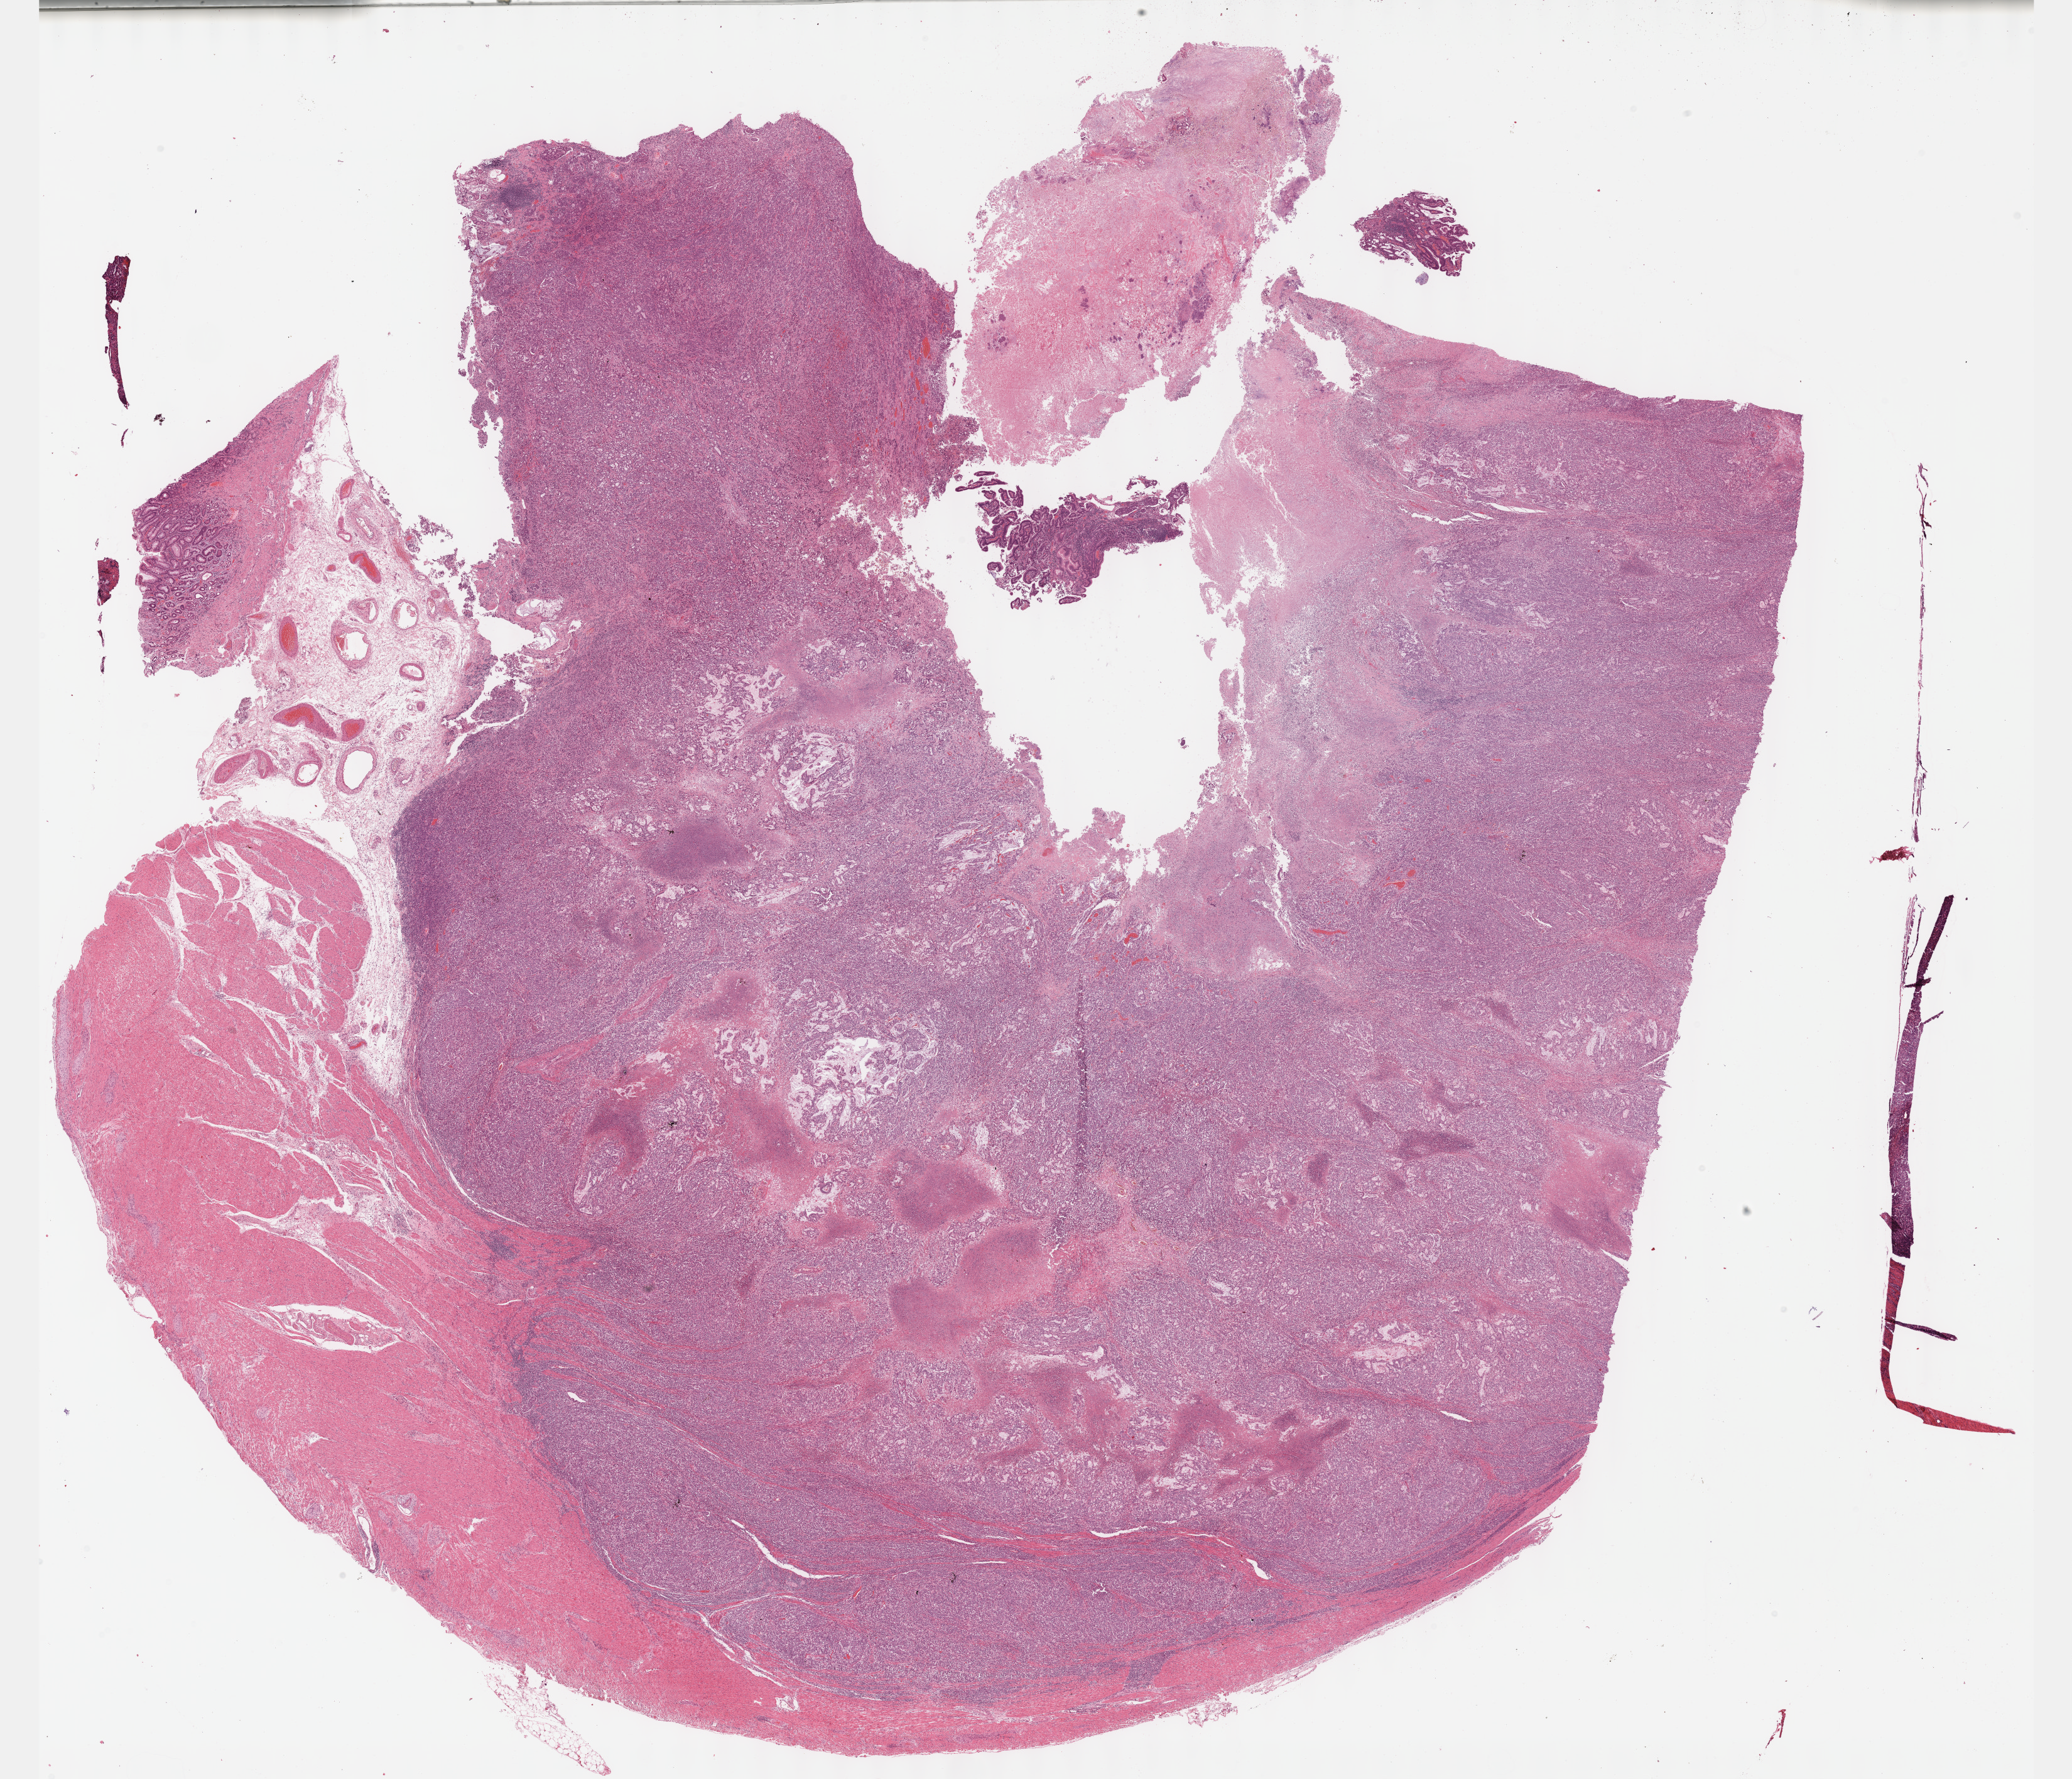
Digitized H&E tissue section (whole slide), low-resolution overview of the scanned area, about 26.7 x 22.9 mm (slide scanned at 40x). Formalin-fixed paraffin-embedded (FFPE) diagnostic section. Primary tumour sample from the stomach. Male, age 68 years at initial diagnosis. Histologic grade: G2 (moderately differentiated).
AJCC pathologic stage: IIIA. Lymph nodes positive (case pathology): 1 of 16 examined. Pathologic diagnosis: Mucinous adenocarcinoma (body of stomach).